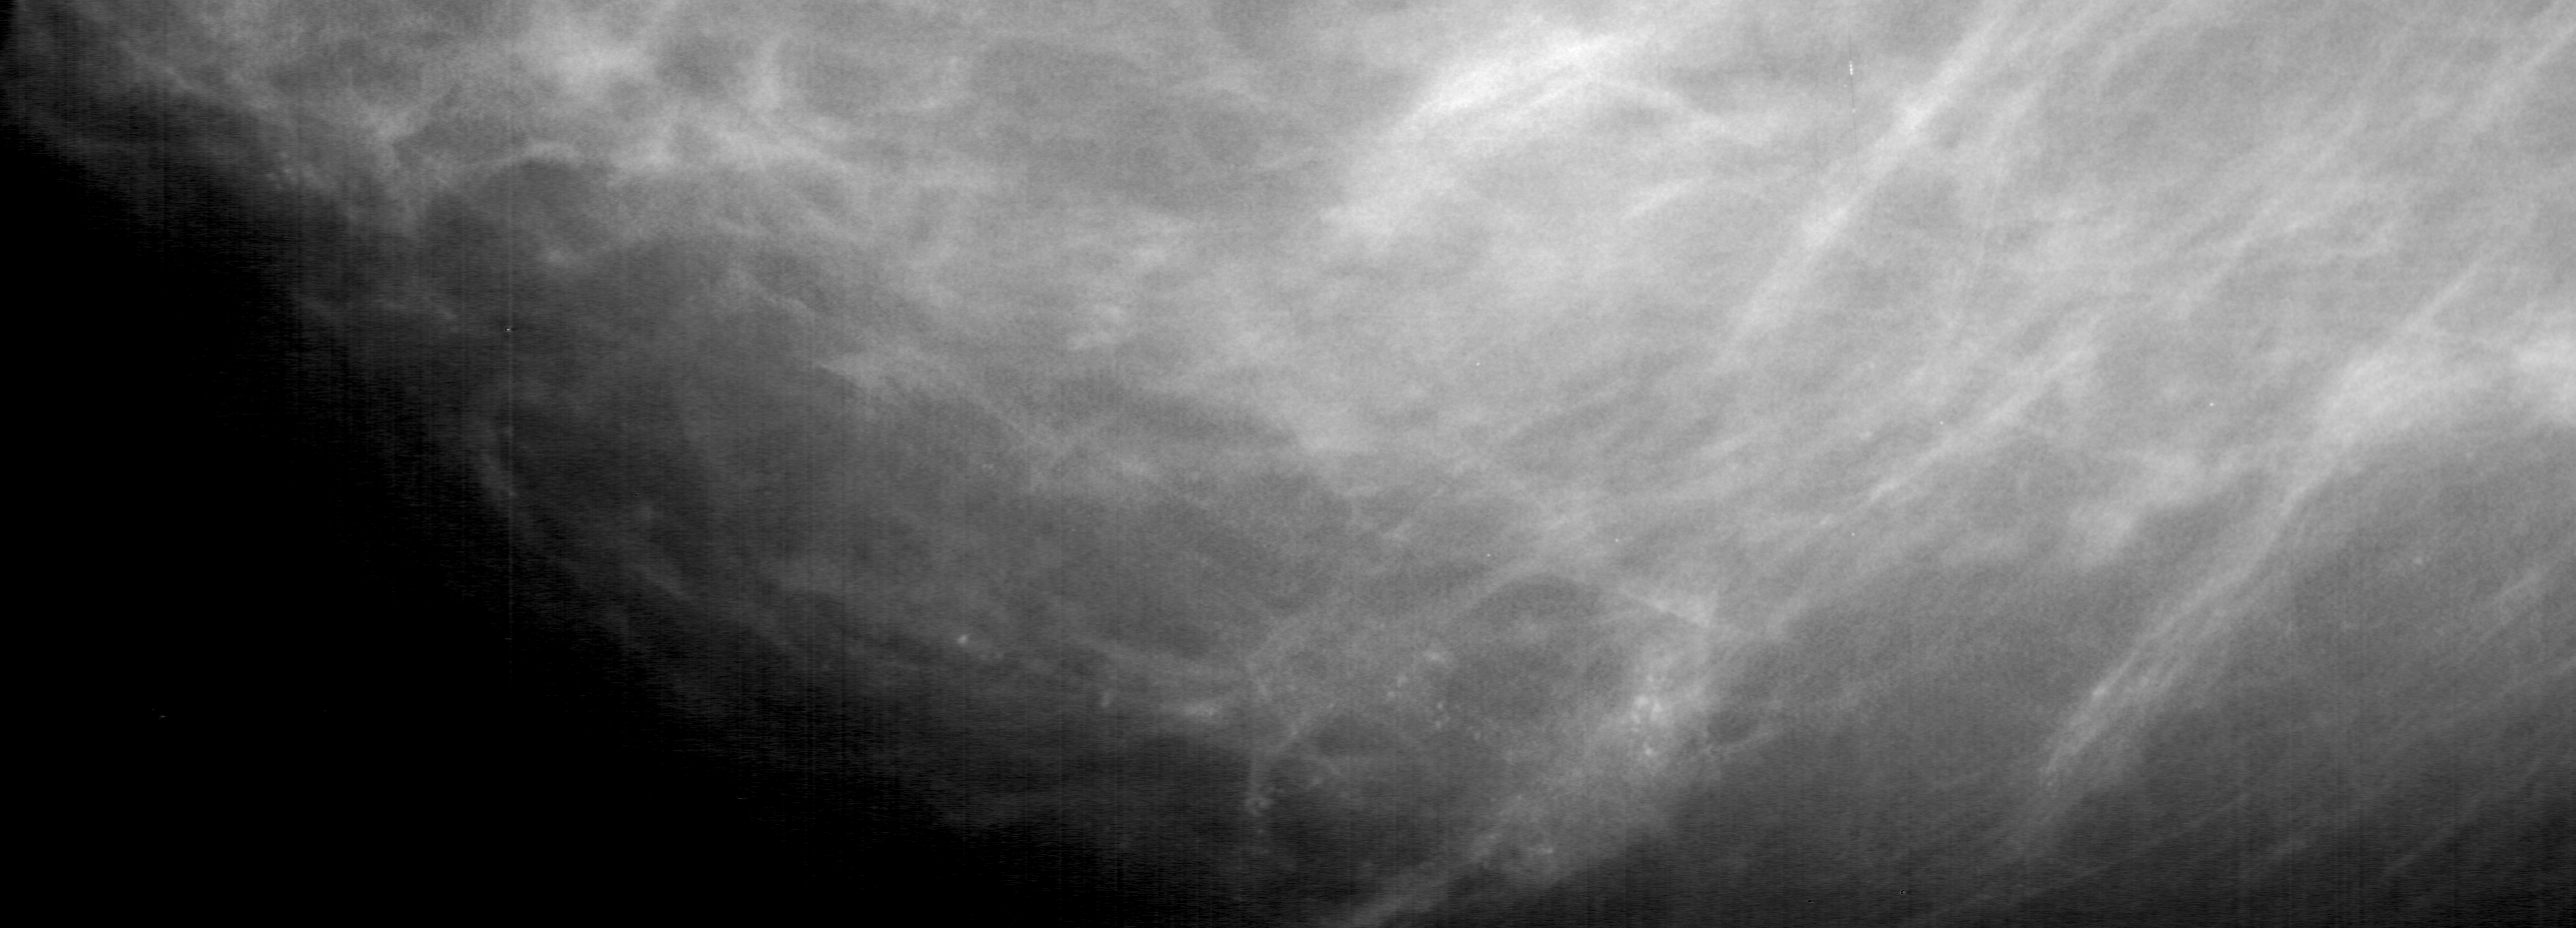
Crop from a digitized film mammogram around one marked abnormality, left breast, MLO view.
- Calcifications, morphology pleomorphic, distribution segmental; BI-RADS assessment category 5; pathology result (as recorded, not read from the image): malignant.